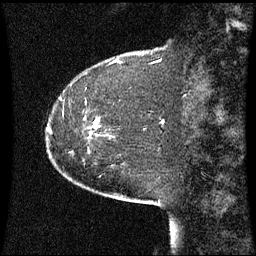
Breast MRI (dynamic contrast-enhanced), one sagittal slice. Position 13 of 60 along the scan axis. Dynamic contrast-enhanced series, image 2 of 3 at this slice position (ordered by acquisition). 1.5 T. TE 4.2 ms, TR 8.9 ms. 2.2 mm slice thickness. 256 × 256 image matrix. Patient: female, 51 years. Case-level facts recorded for this patient, not image findings: setting: breast cancer imaged before/during neoadjuvant chemotherapy; receptor status: HR-positive, HER2-negative.
Outlined on this slice (semi-automatically segmented with operator editing):
- analysis volume of interest (the breast-tissue region the enhancement analysis was run in; not a lesion): bounding box <90,118,99,133> (left, top, right, bottom; pixels)
- tumour enhancement mask (voxels above the 70 % enhancement threshold inside the analysis volume of interest): <94,120,99,127>